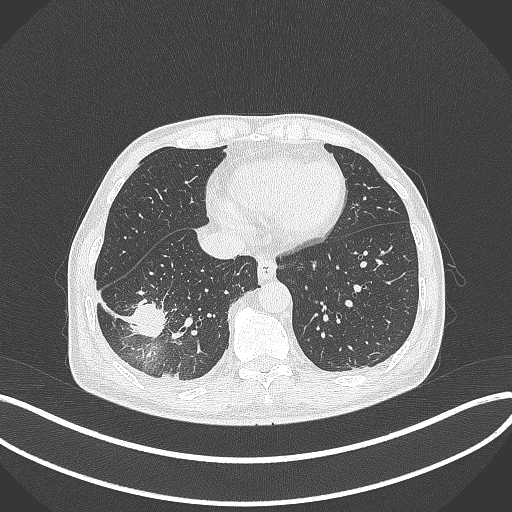
Chest CT, one axial slice. 120 kVp. Lung window (W 1500 / L -600 HU). 512 × 512 image matrix. Patient: male, 64 years. From the clinical record (not read from this slice): clinical TNM (as recorded): T3 N0 M0; histopathological grade: G2-3.
Outlined on this slice (bounding box drawn by a radiologist):
- lung tumour (recorded histology: adenocarcinoma): bounding box [x1, y1, x2, y2] px = [125, 297, 169, 342]